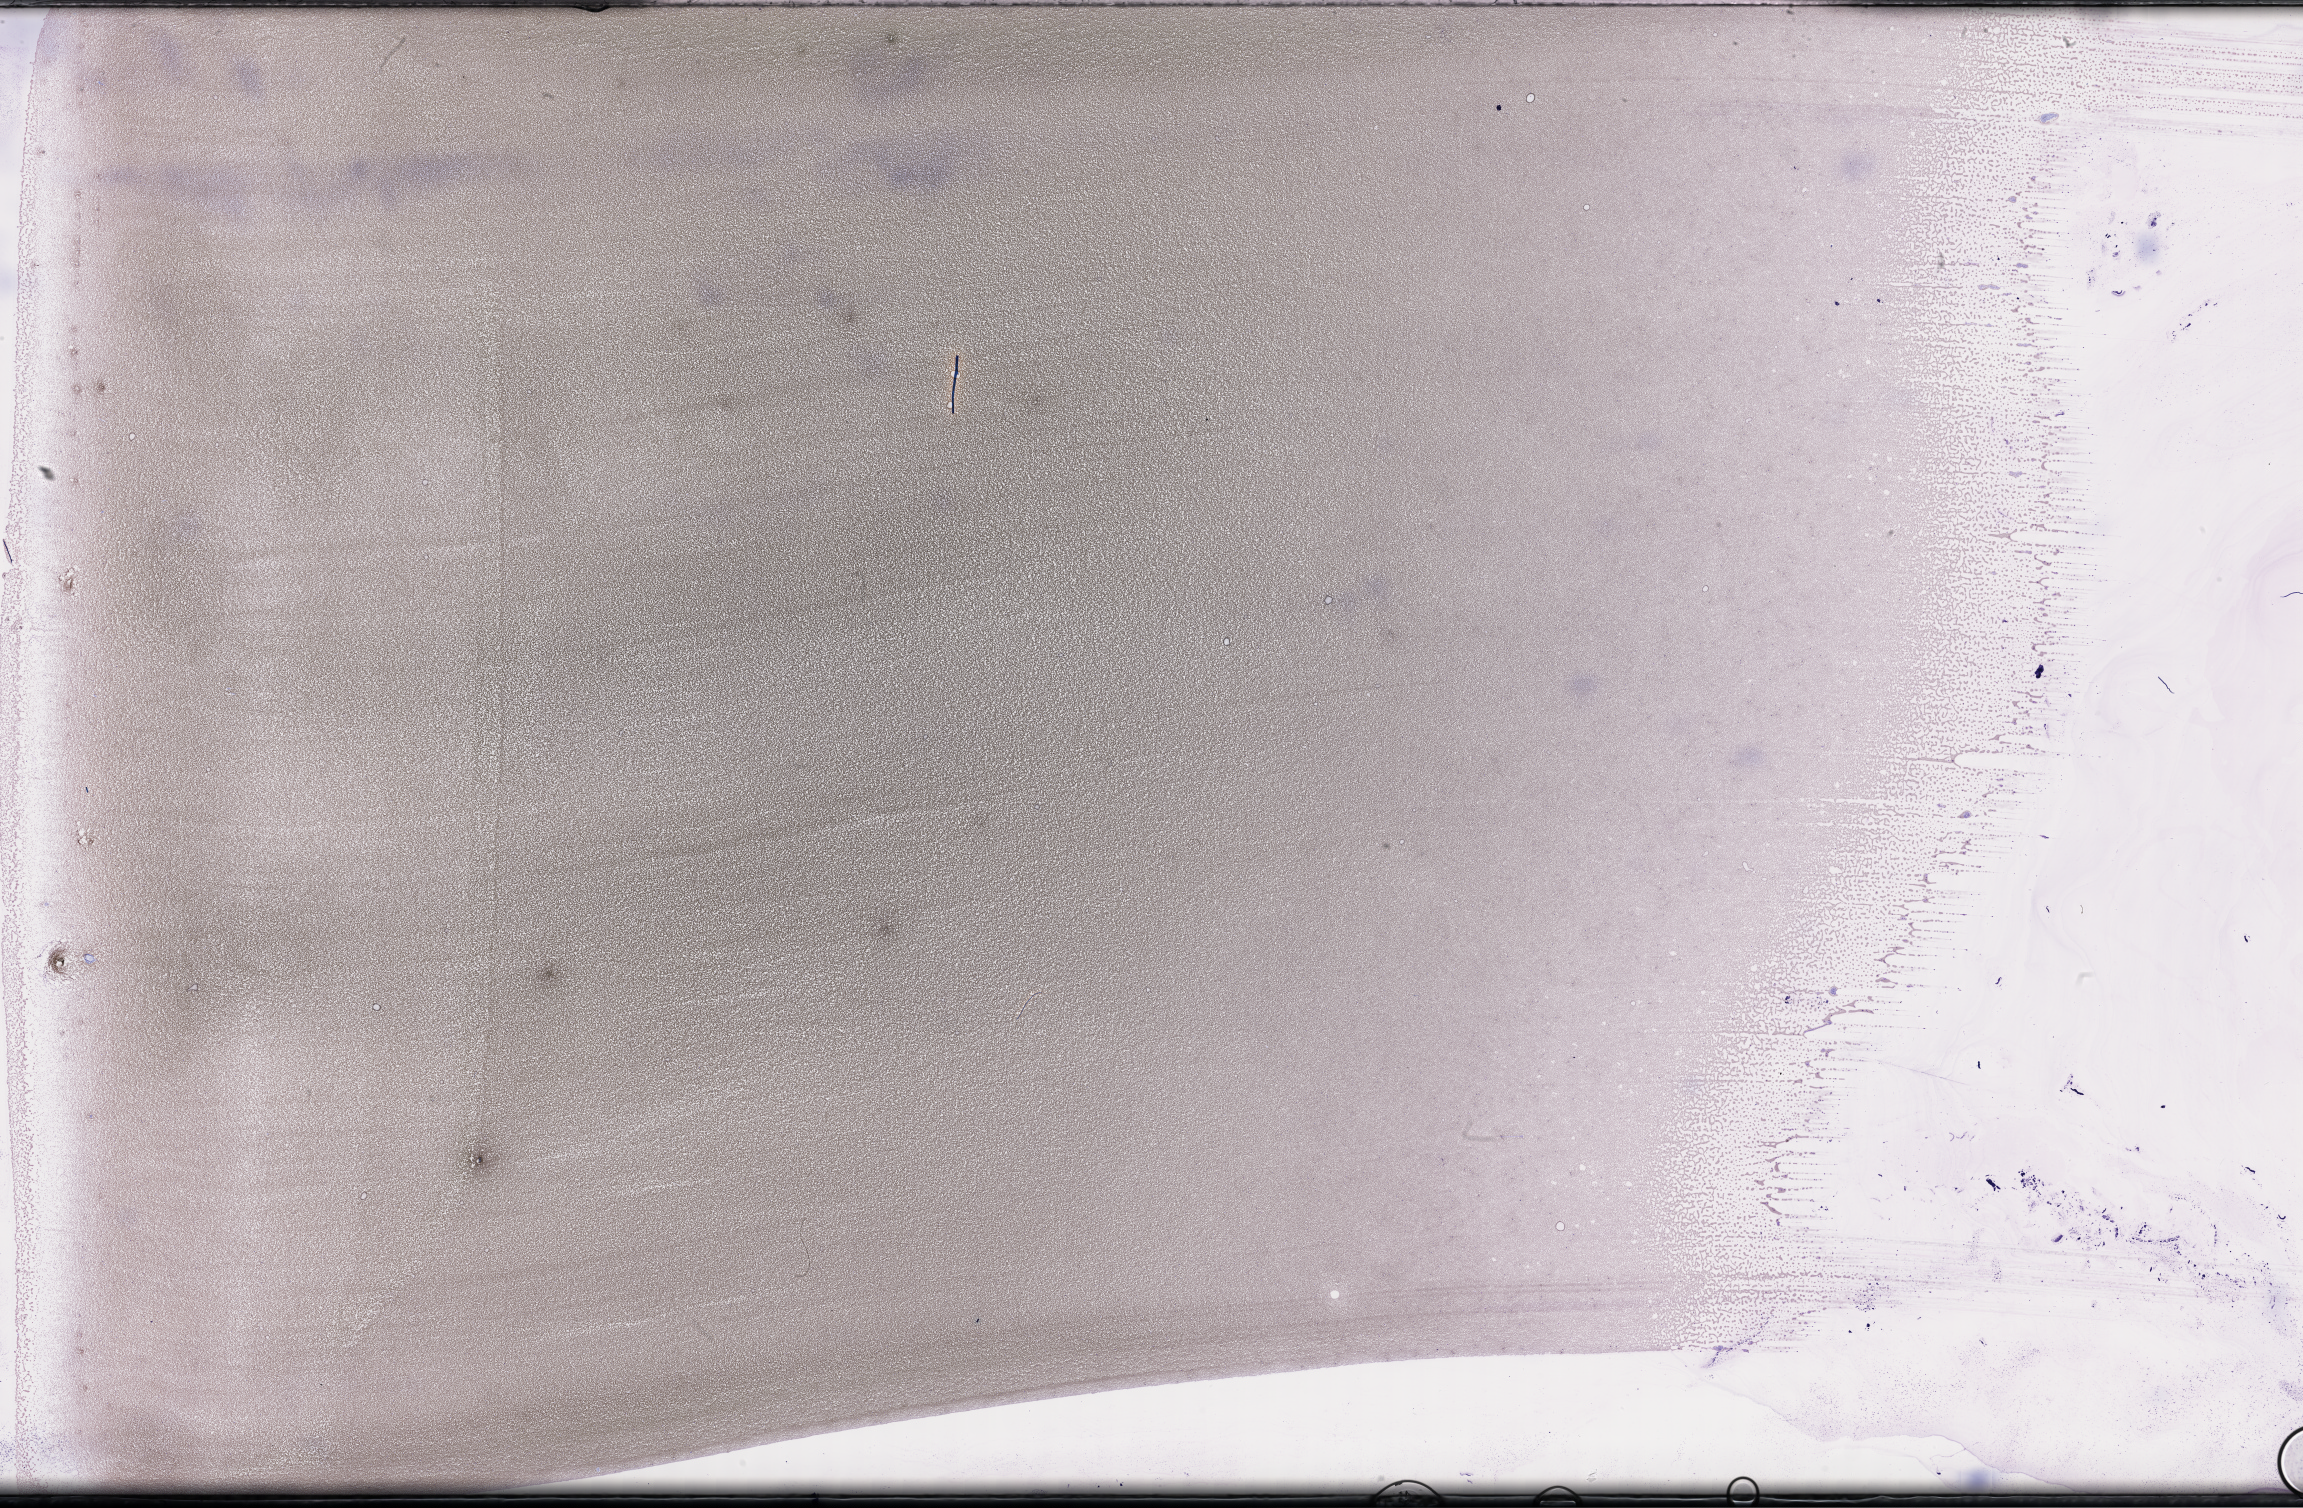
Whole-slide image of a whole blood smear, Wright–Giemsa stain — whole scanned area (about 37.2 x 24.4 mm) shown as a low-resolution overview, EDTA-anticoagulated smear, collected on treatment. Patient: female.
Patient diagnosis: Plasma Cell Myeloma.